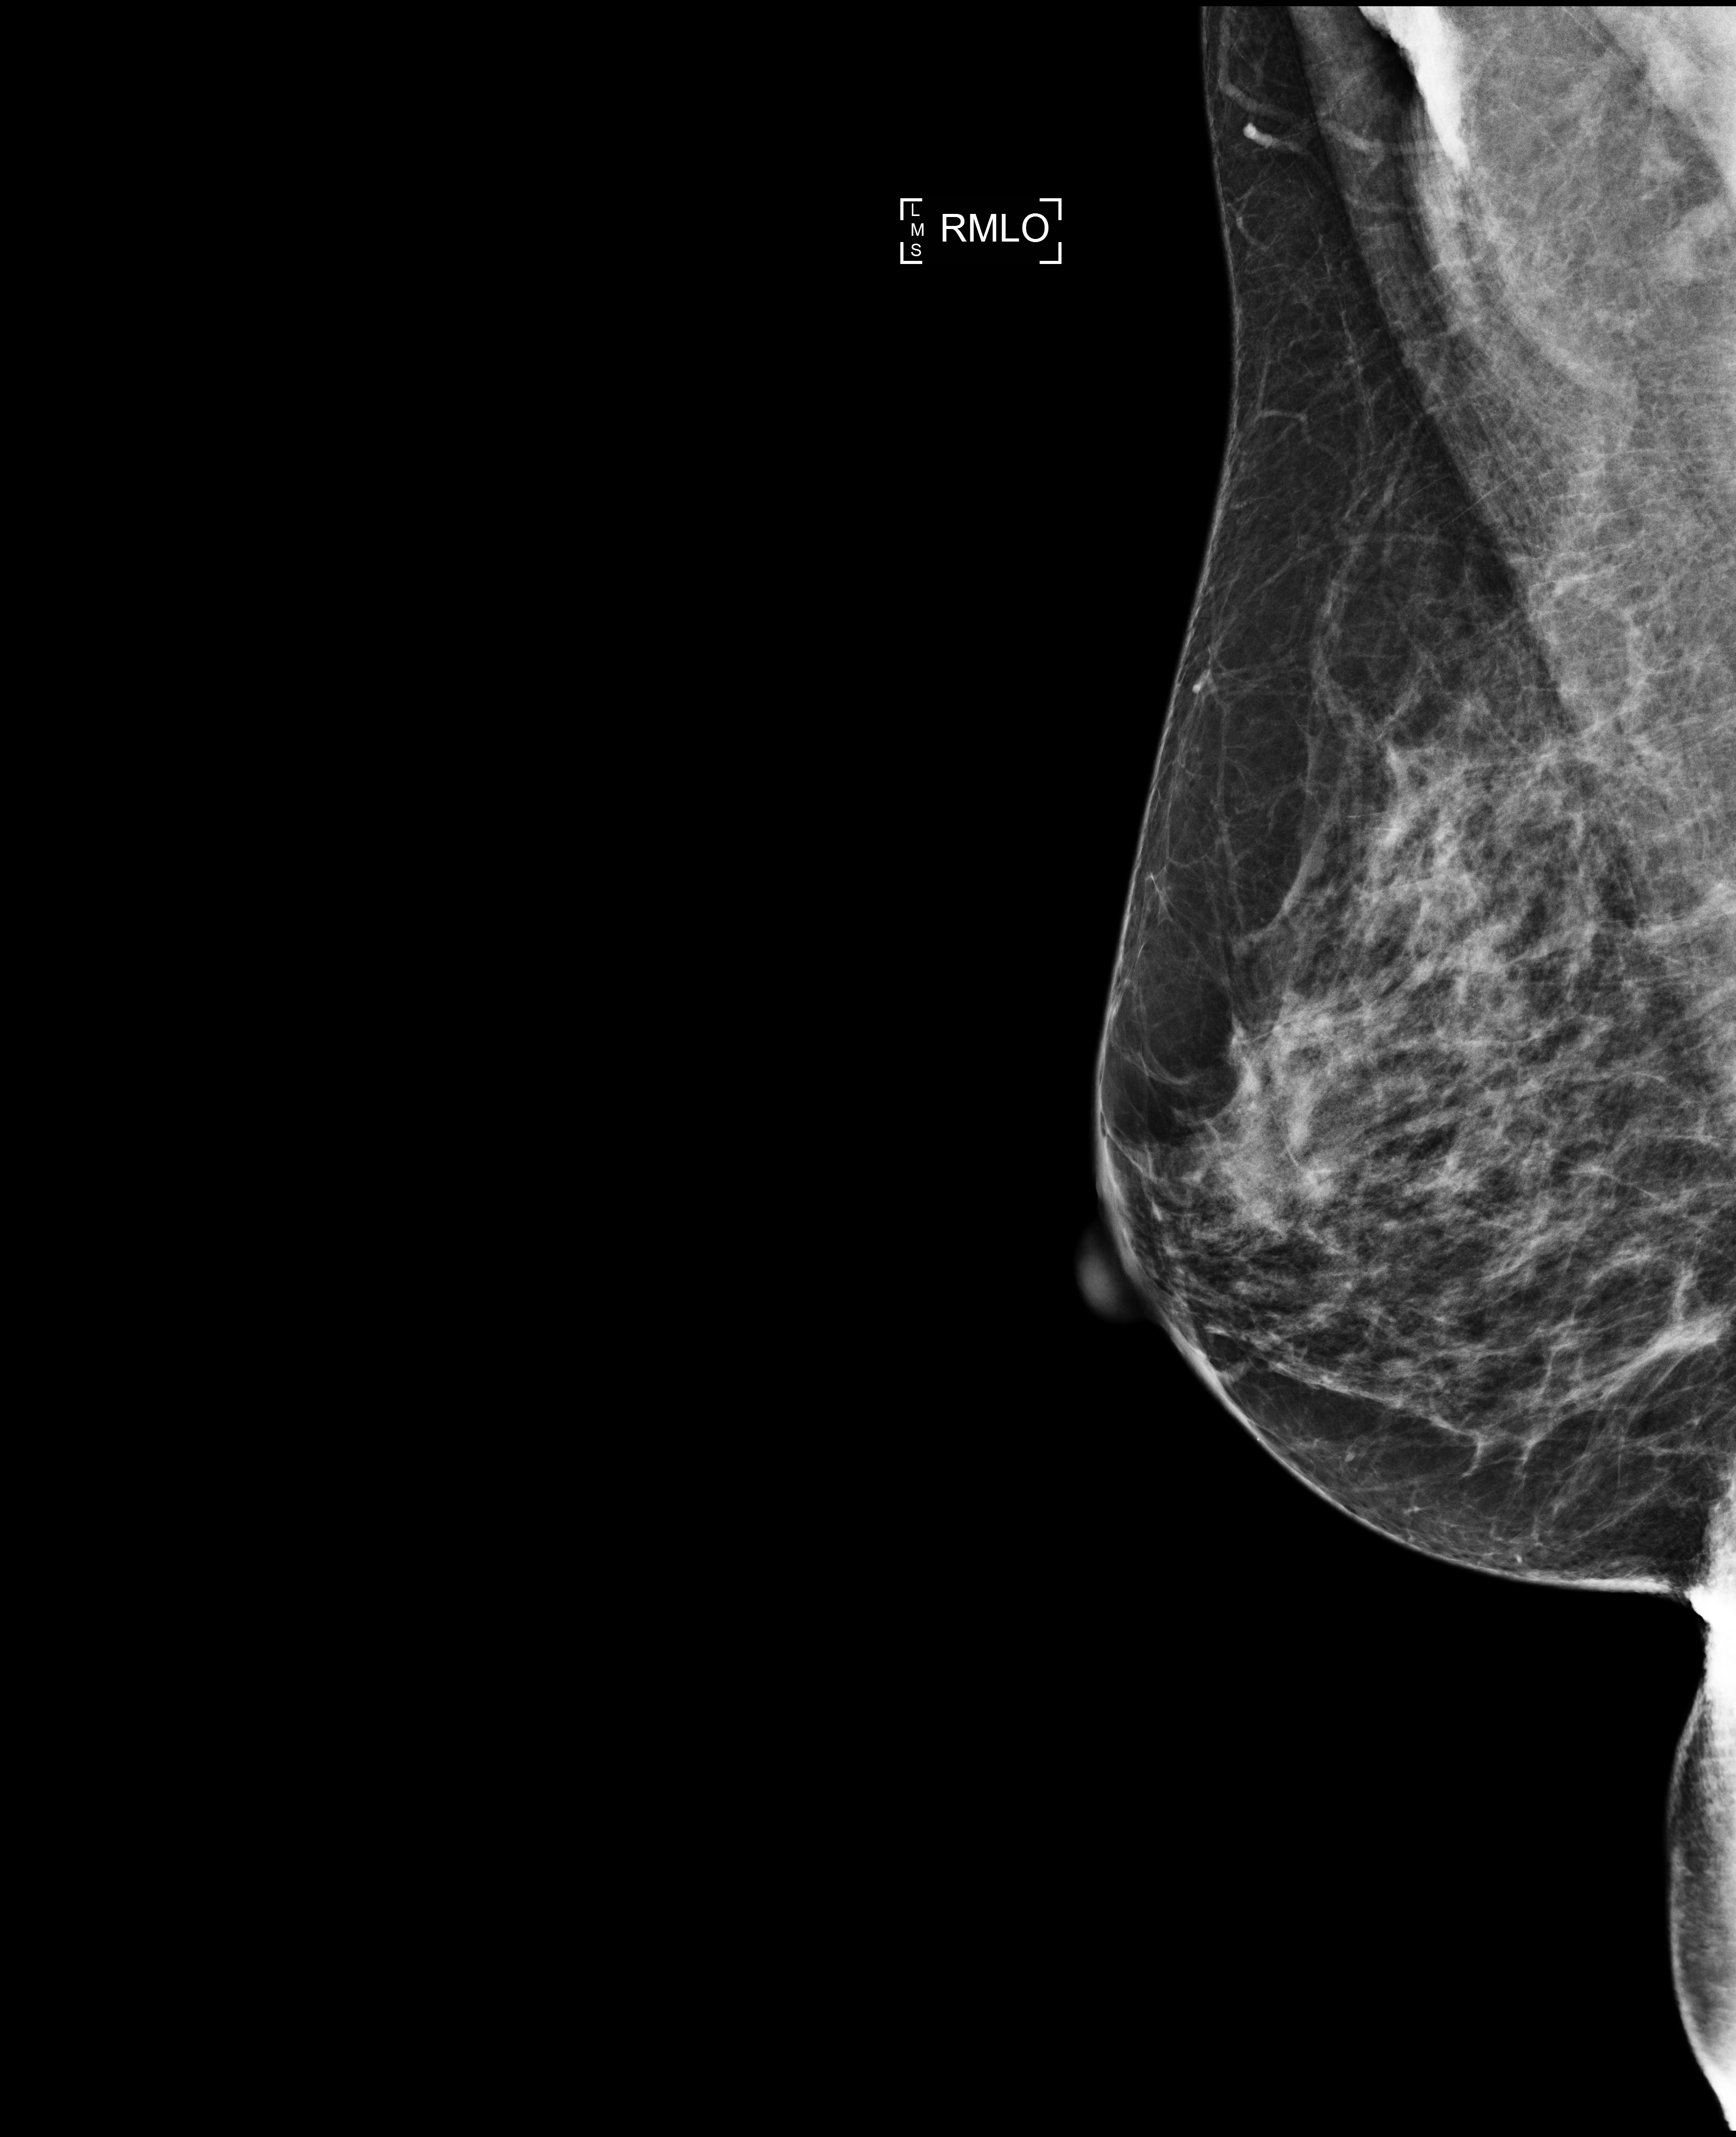
Digital mammogram (FFDM); right breast; mediolateral oblique (MLO) view; annual screening mammography examination. Patient: female, 59 years.
- BI-RADS breast density category at the screening exam (both breasts, scale 1–4): 3
- final BI-RADS assessment for this screening round (tomosynthesis exam, both breasts): category 1
- recall: no recall after this screen